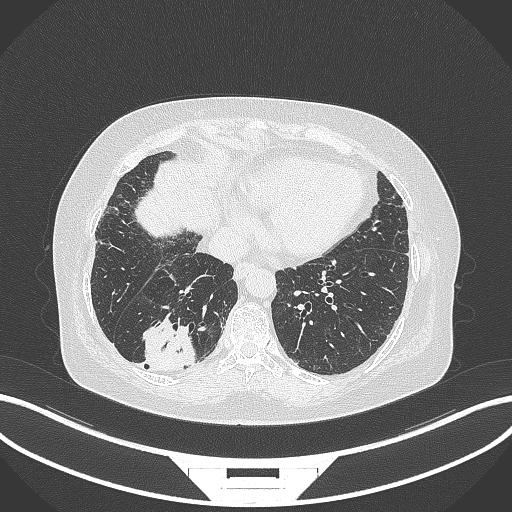
Chest CT, one axial slice. Slice 62 of 296 in the series (ordered by position). Reconstruction kernel B70f. 120 kVp. Lung window (W 1500 / L -600 HU). 1 mm slice thickness. 512 × 512 image matrix, field of view 400 × 400 mm. Patient: female, 65 years. From the clinical record (not read from this slice): clinical TNM (as recorded): T2b N1 M0.
Structures marked on this image (bounding box drawn by a radiologist):
- lung tumour (recorded histology: adenocarcinoma): bounding box (x1, y1, x2, y2) in pixels: (138, 316, 199, 372)